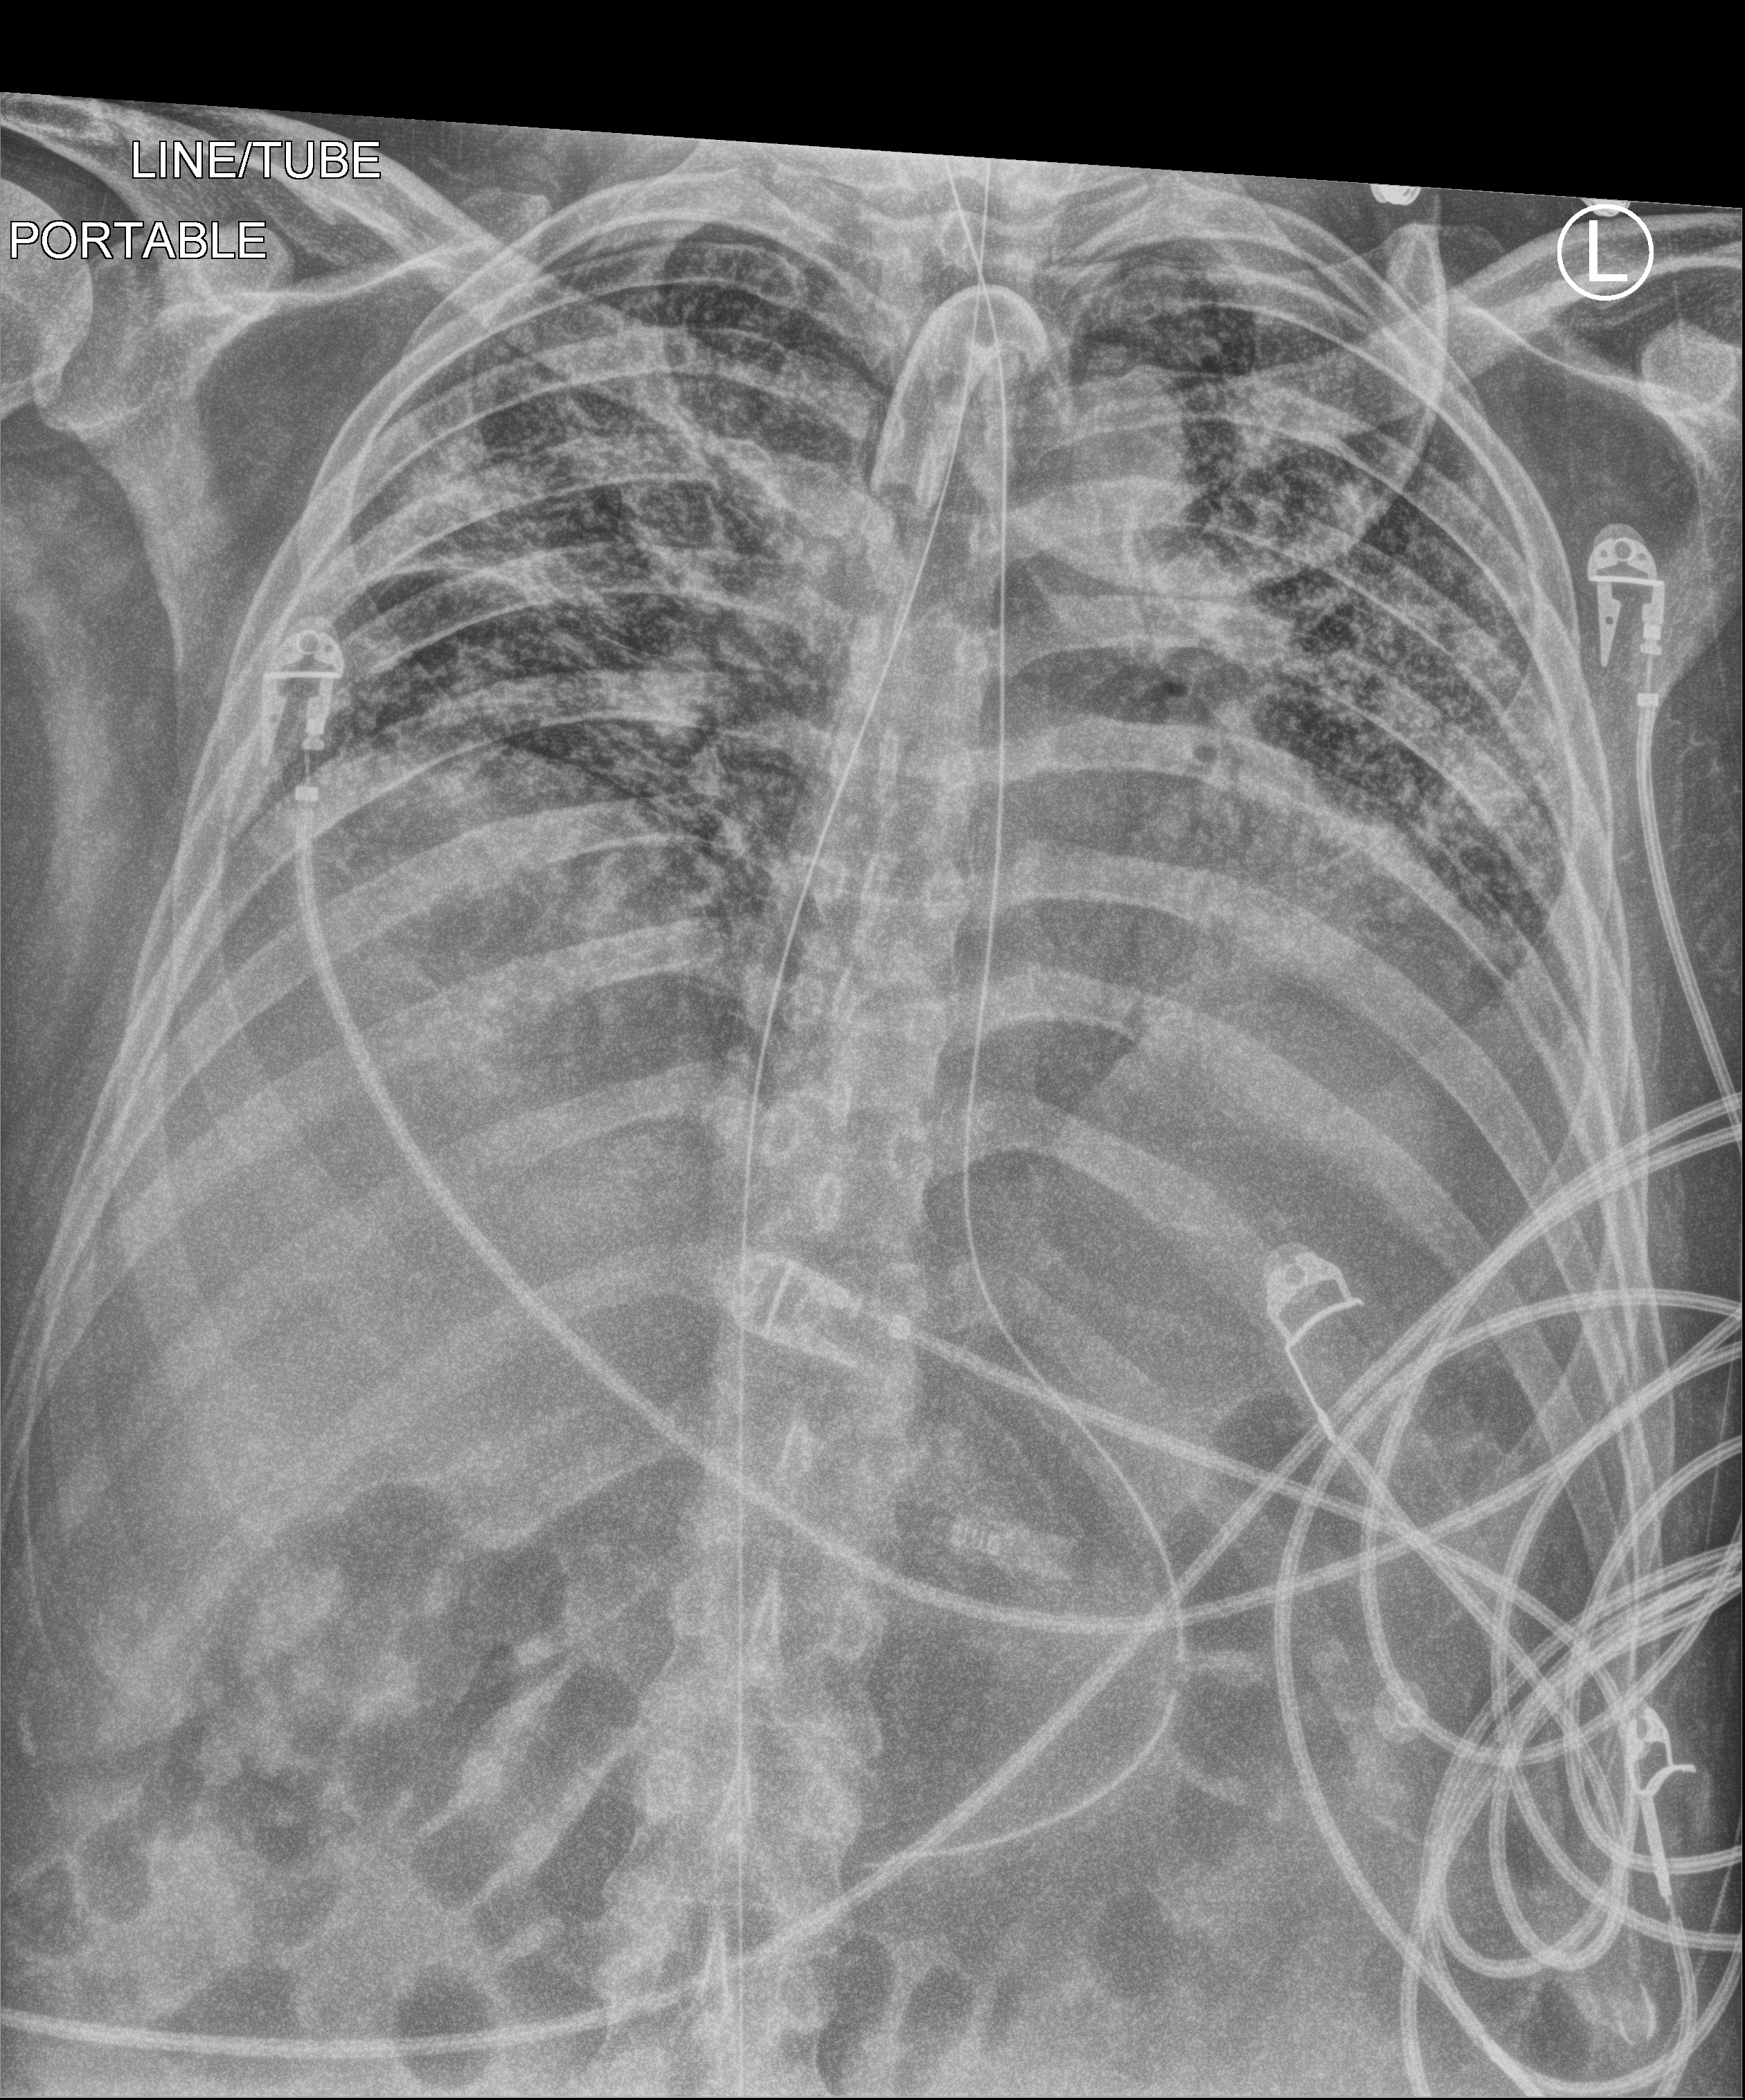
Bedside chest radiograph (computed radiography); anteroposterior (AP) projection. Patient hospitalised with COVID-19; male, aged 18–59 years.
From the hospital-stay record, not from the radiograph (when in the stay this image was taken is not recorded): admitted to intensive care during this hospital stay: yes.